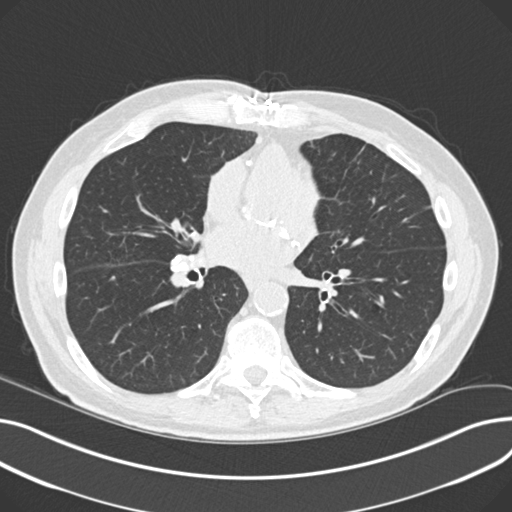
Low-dose screening chest CT, one axial slice; position 101 of 230 along the scan axis; reconstruction kernel B30f; 120 kVp; lung window (W 1500 / L -600 HU); 2 mm slice thickness; 512 × 512 image matrix, field of view 372 × 372 mm.
Structures marked on this image (manually delineated by an expert):
- lesion 2 (tumor, lower lobe of right lung): bounding box [x1, y1, x2, y2] px = [109, 275, 116, 281]